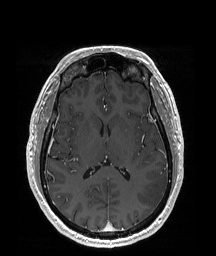
Brain MRI from a brain-tumour surgery series, one axial slice; position 94 of 192 along the scan axis; T1-weighted post-contrast; 1 mm slice thickness; 216 × 256 image matrix, field of view 219 × 260 mm. Case-level facts recorded for this patient, not image findings: histopathology: Glioblastoma; WHO grade: 4; IDH mutation: no.
Outlined on this slice (expert manual segmentation):
- tumour: bounding box <137,172,168,210> (left, top, right, bottom; pixels)